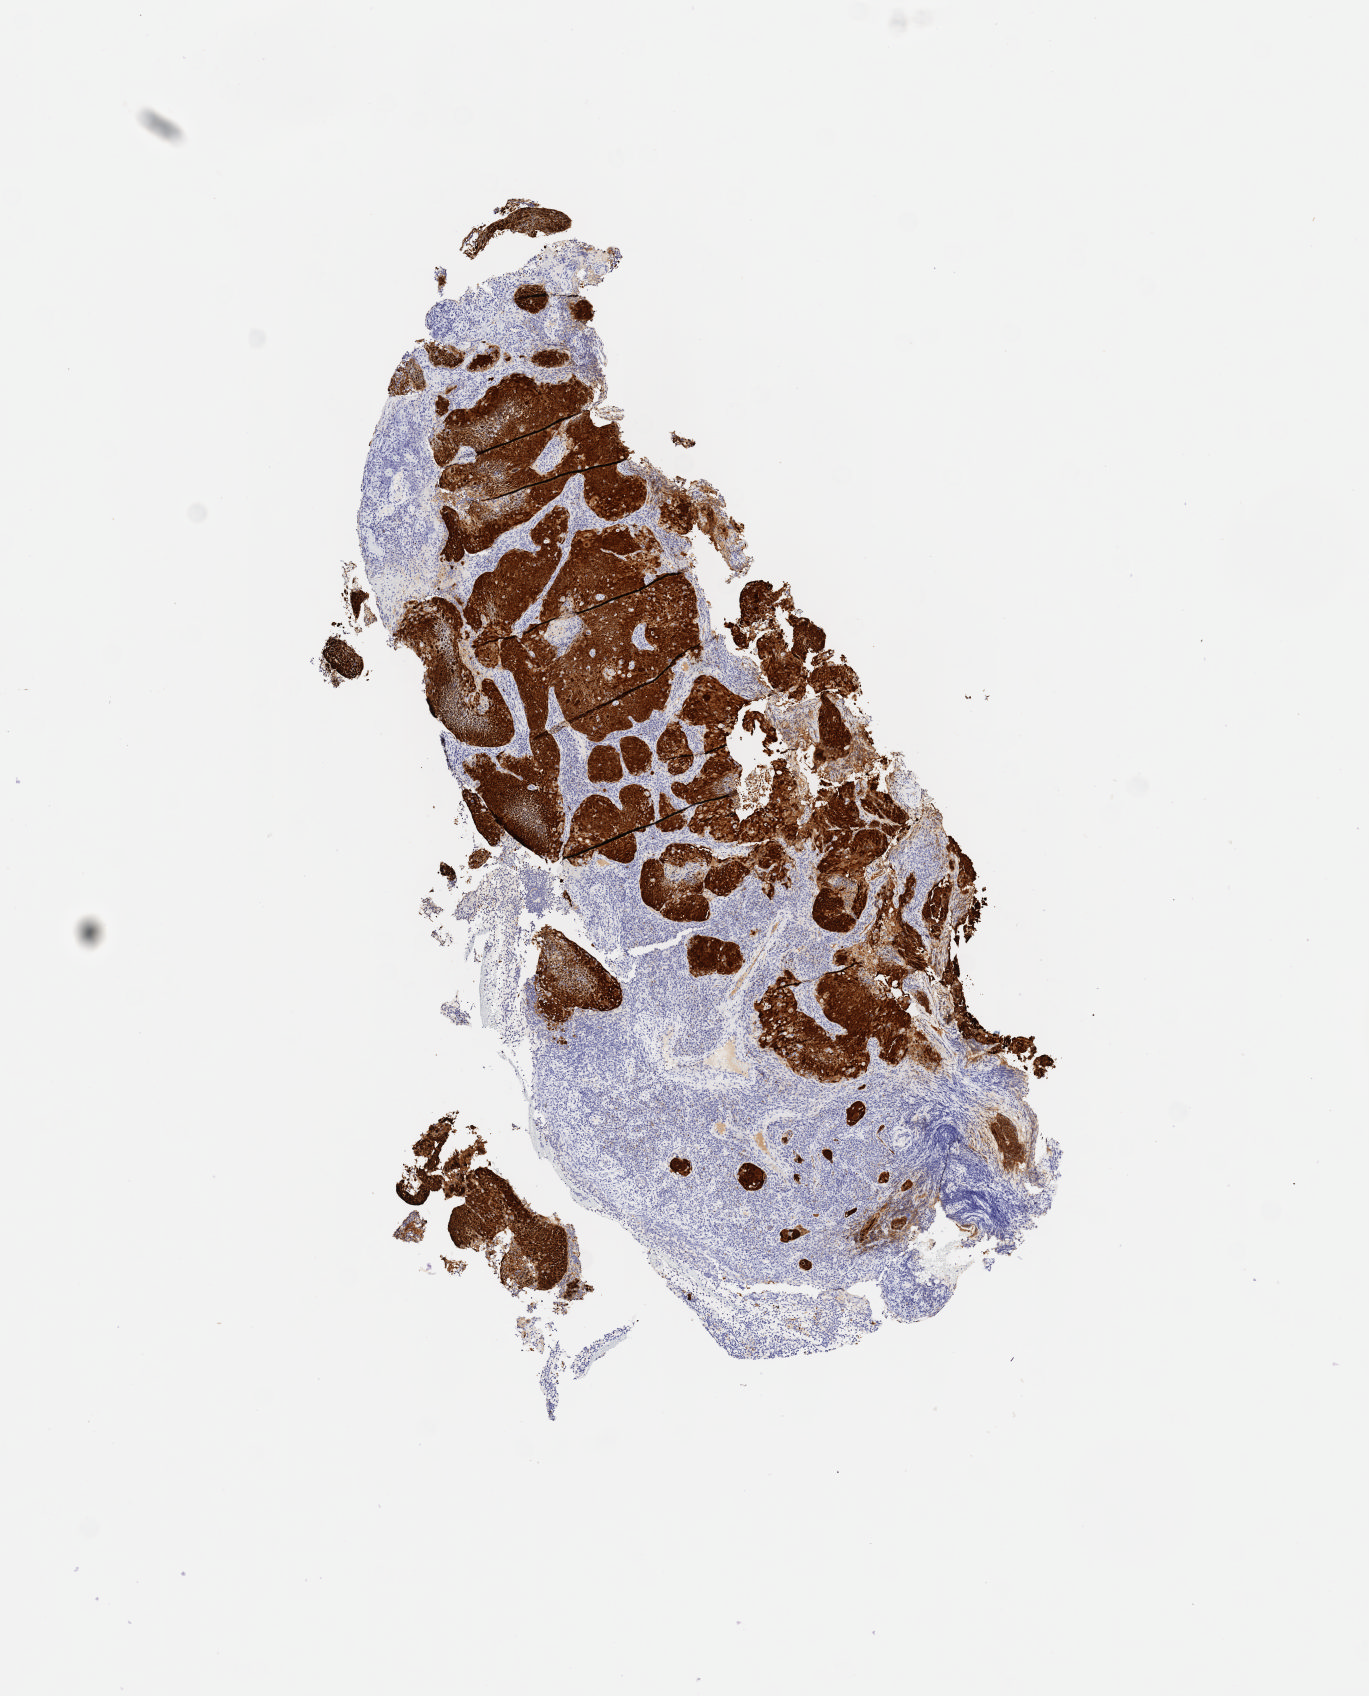
IHC for p16 (p16INK4a), whole-slide image — shown as a low-resolution overview of the whole scanned area (about 5.5 x 6.9 mm), specimen: tumor tissue, anatomic site: cervix. Patient: female, age 42 years.
* diagnosis: Squamous cell carcinoma, large cell, nonkeratinizing, NOS